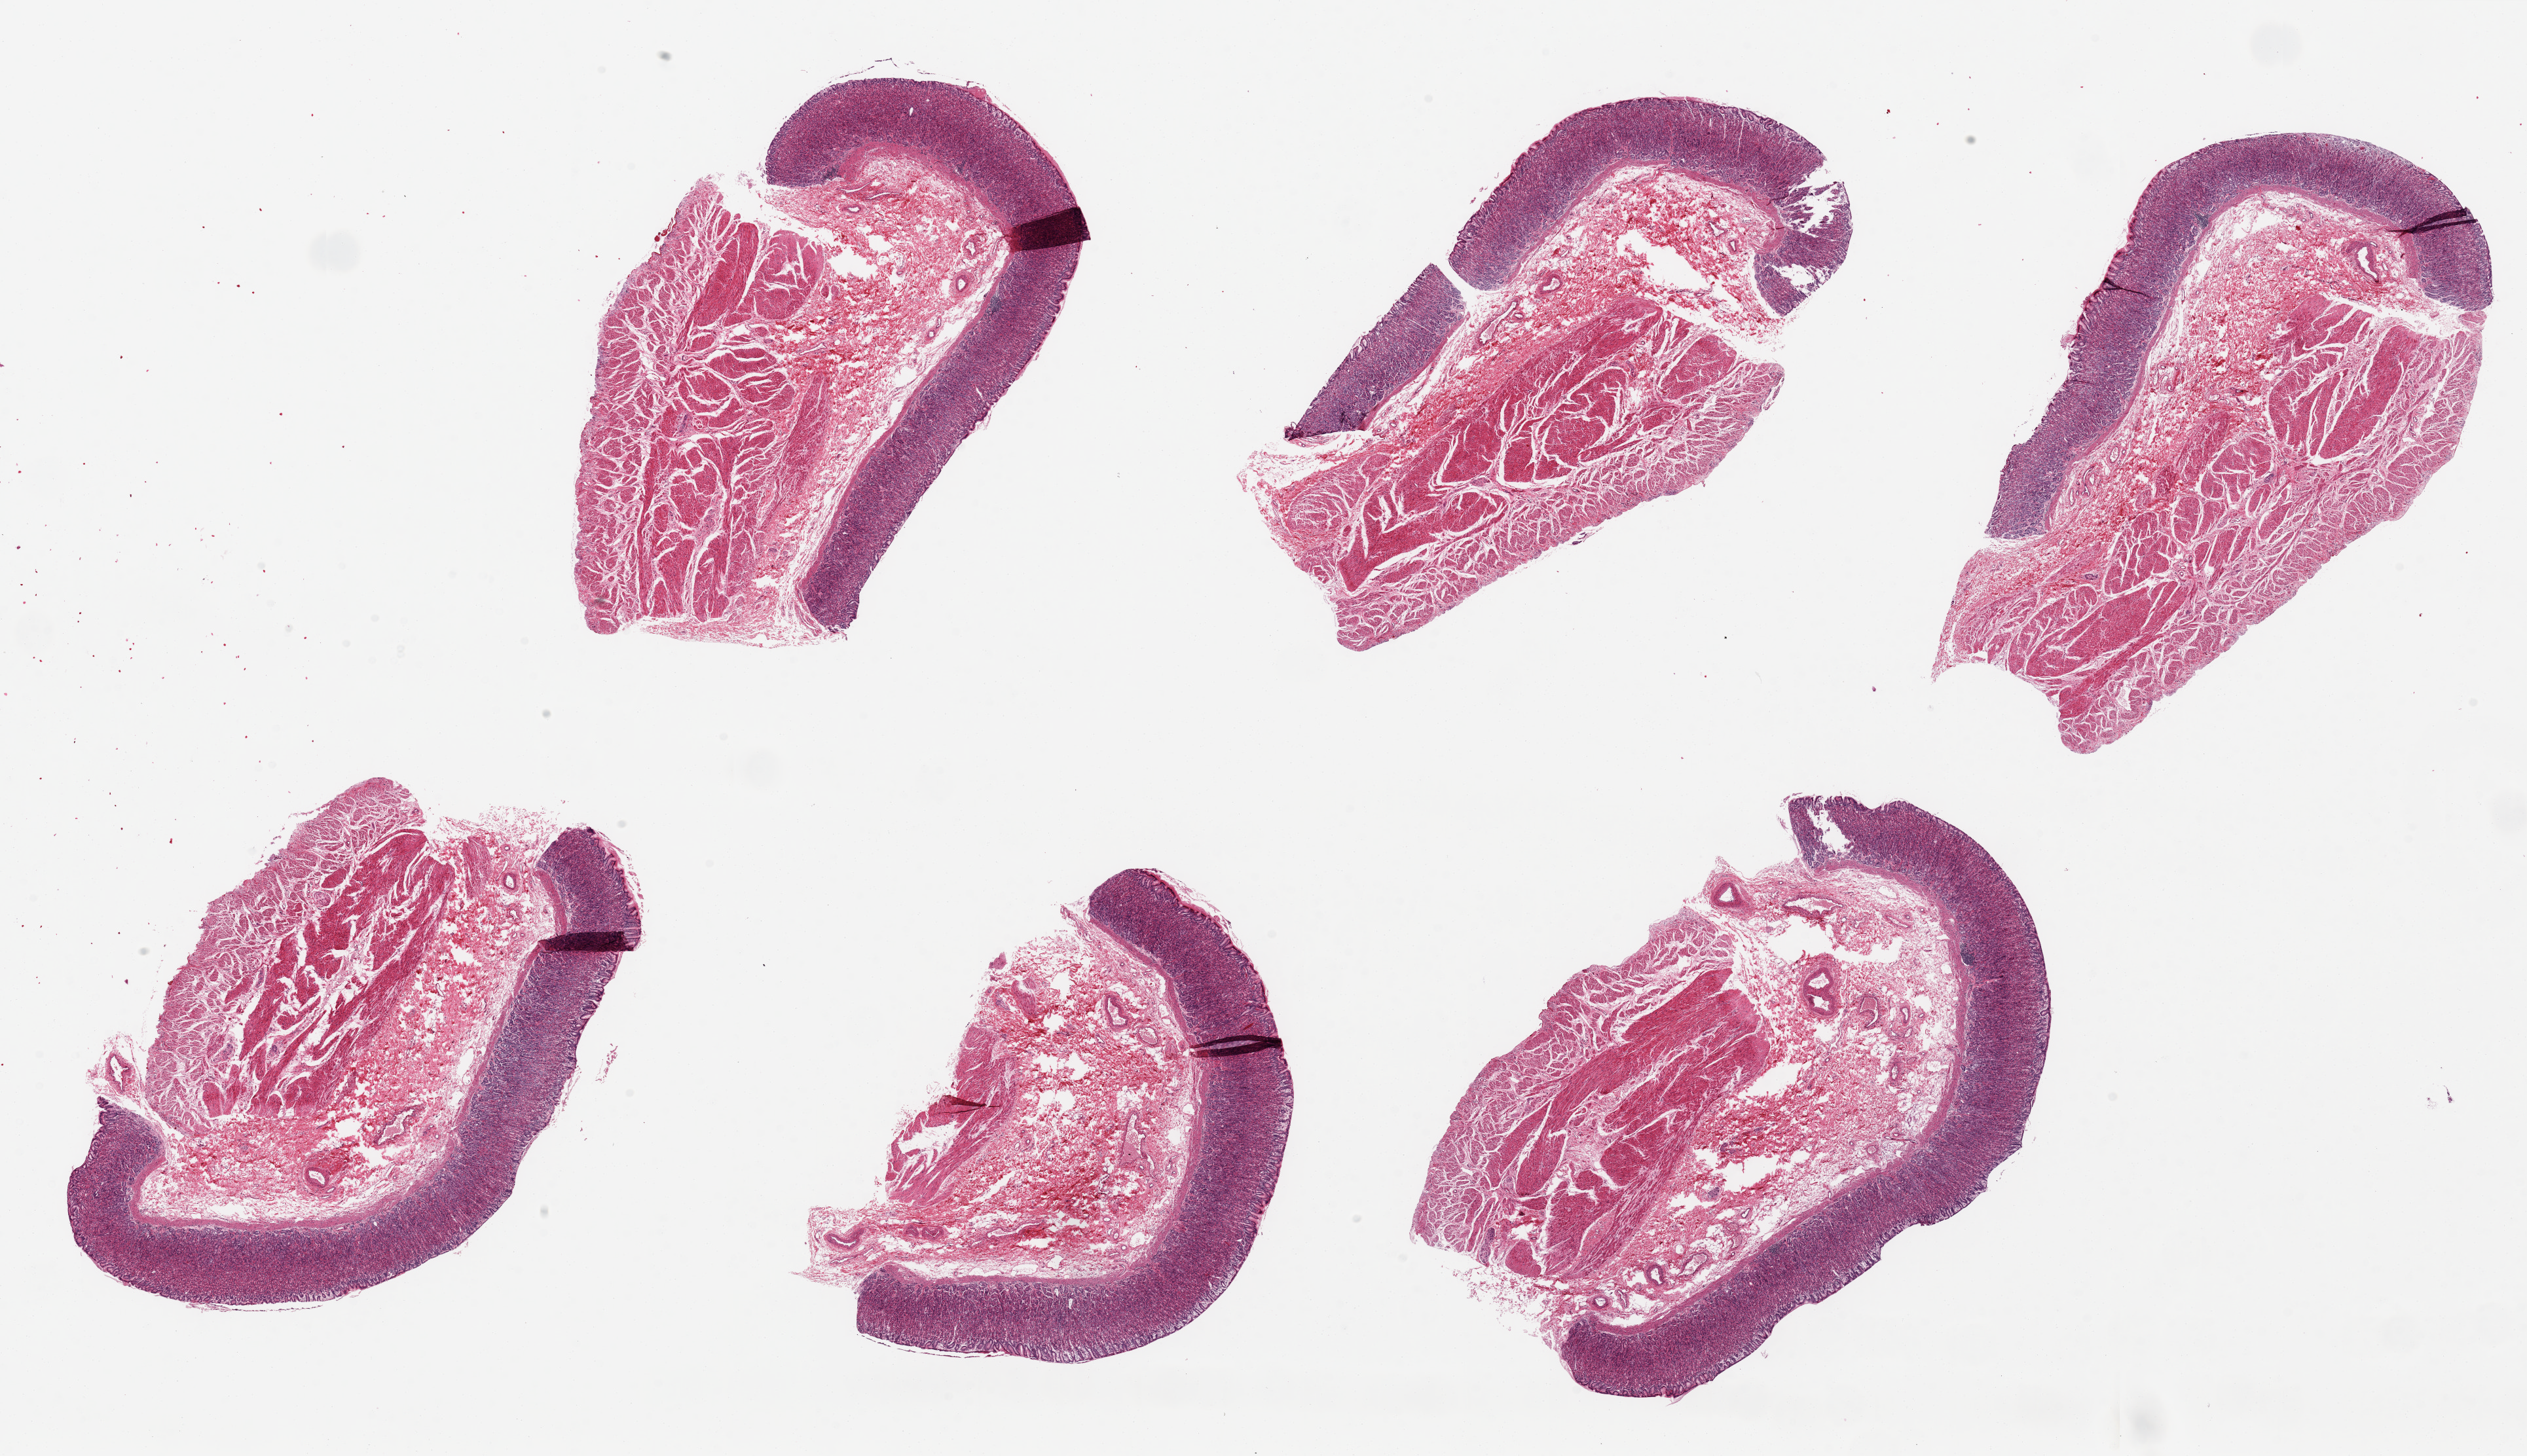
Hematoxylin and eosin (H&E) whole-slide image, a low-resolution overview of the entire scanned area, about 30.5 x 17.6 mm; PAXgene-fixed, paraffin-embedded tissue; target tissue: stomach; tissue donor sample. Male donor.
* review note (as recorded): 6 pieces up to 8x5 mm; very good mucosal preservation